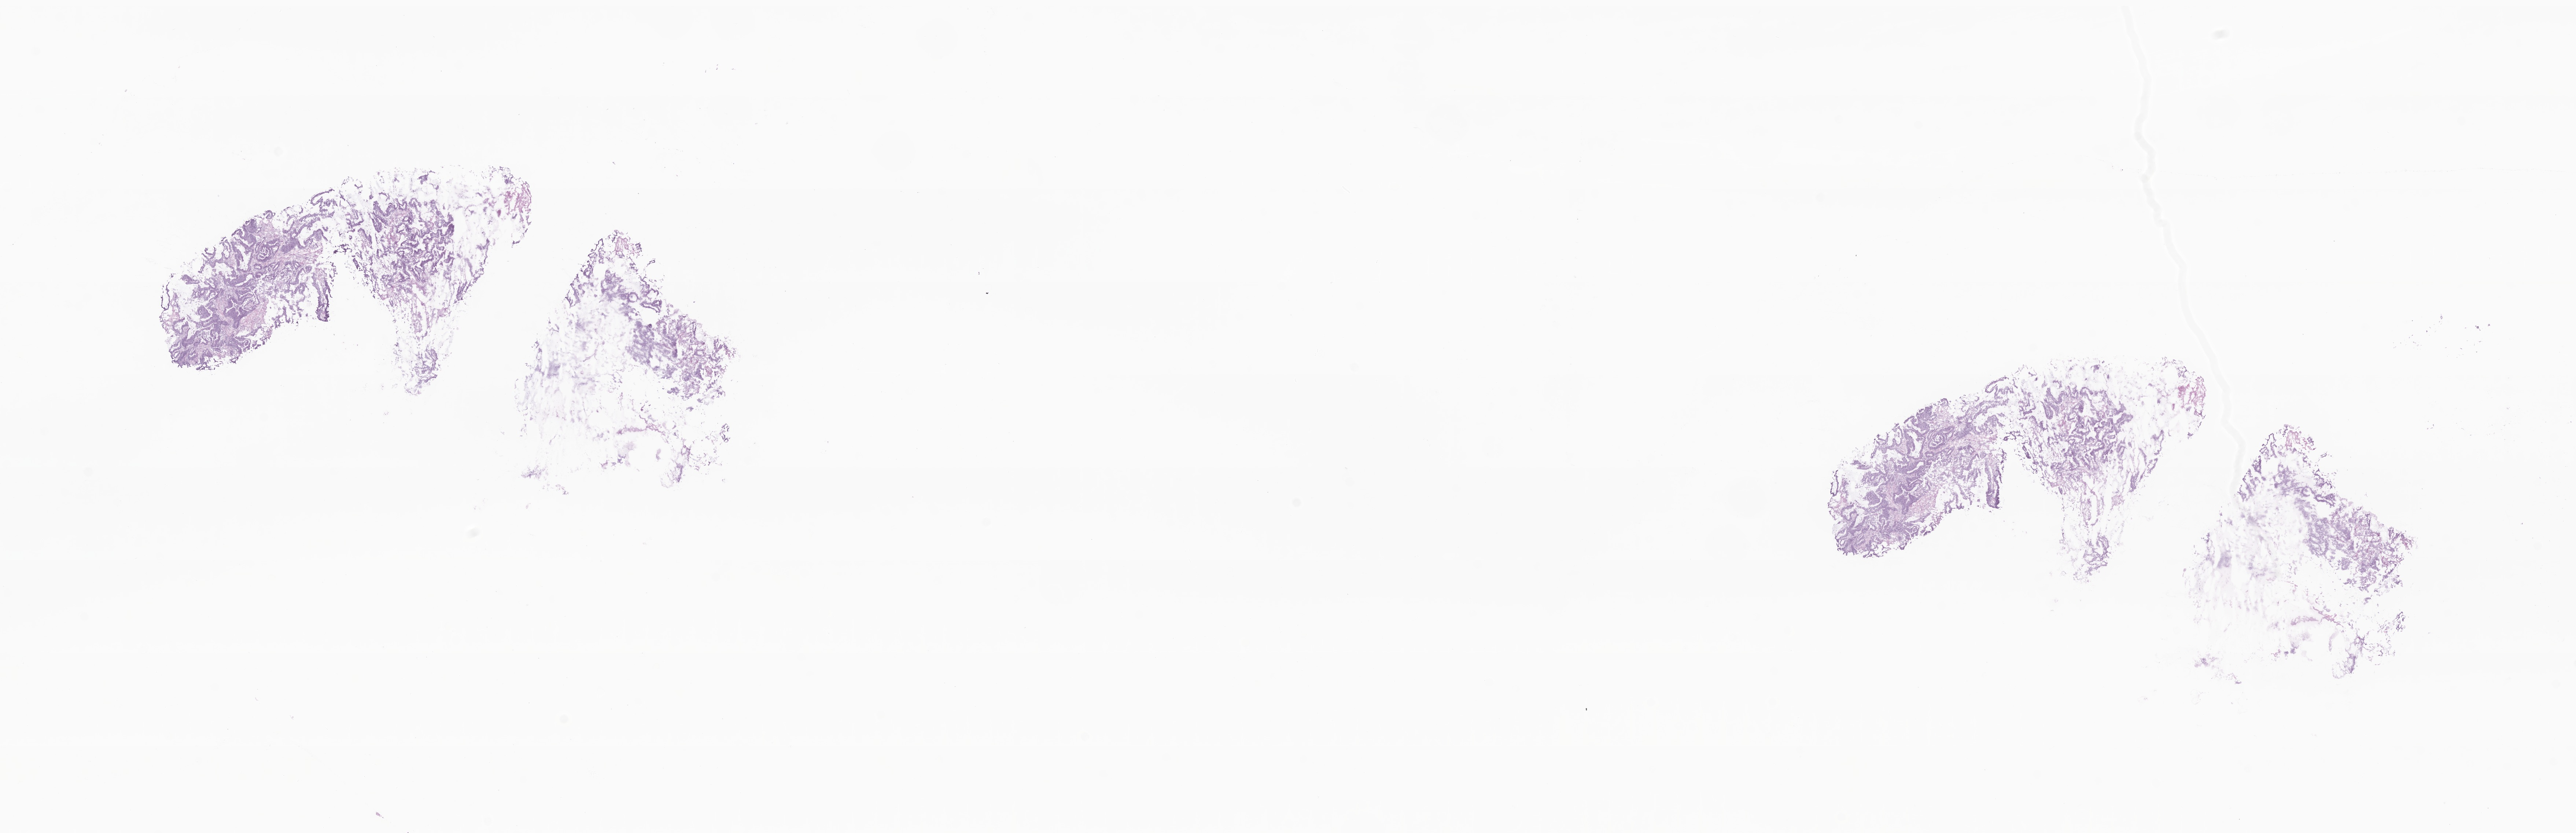
Whole-slide image, H&E stain — a low-resolution overview of the entire scanned area, about 29.6 x 9.6 mm; frozen section; specimen: primary tumor; site: ascending colon. Male, age 75 years at initial diagnosis. Slide review estimates, as recorded: tumor cells 85%, tumor nuclei 85%, stromal cells 15%, necrosis 0%, normal cells 0%. Inflammatory infiltration, as recorded: lymphocyte infiltration 3%, monocyte infiltration 1%, neutrophil infiltration 5%.
Histologic diagnosis: Adenocarcinoma, NOS.